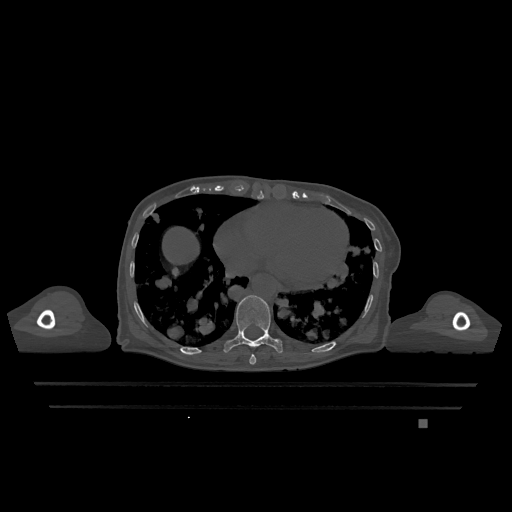
CT including the spine, one axial slice. Position 646 of 1317 along the scan axis. Bone window (W 1800 / L 400 HU). 512 × 512 image matrix, field of view 500 × 500 mm. Patient: female, 74 years. From the clinical record (not read from this slice): primary cancer: lung; vertebrae with lytic lesions (as recorded): T1, T4, T5, T6, L4, L5.
Annotated regions visible in this slice (semi-automatically segmented with operator editing):
- T10 vertebra: bounding box (x1, y1, x2, y2) in pixels: (223, 295, 283, 353)
- T9 vertebra: (249, 354, 256, 365)